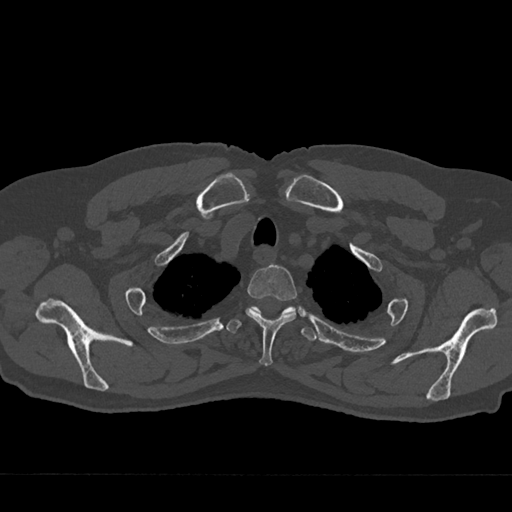
CT including the spine, one axial slice. Slice 600 of 797 in the series (ordered by position). 120 kVp. Bone window (W 1800 / L 400 HU). 0.5 mm slice thickness. 512 × 512 image matrix, field of view 377 × 377 mm. Patient: male, 75 years. Case-level facts recorded for this patient, not image findings: primary cancer: renal.
Annotated regions visible in this slice (semi-automatic segmentation, software-assisted and operator-edited):
- T2 vertebra: bounding box (x1, y1, x2, y2) in pixels: (246, 264, 297, 366)
- T3 vertebra: (226, 306, 317, 341)